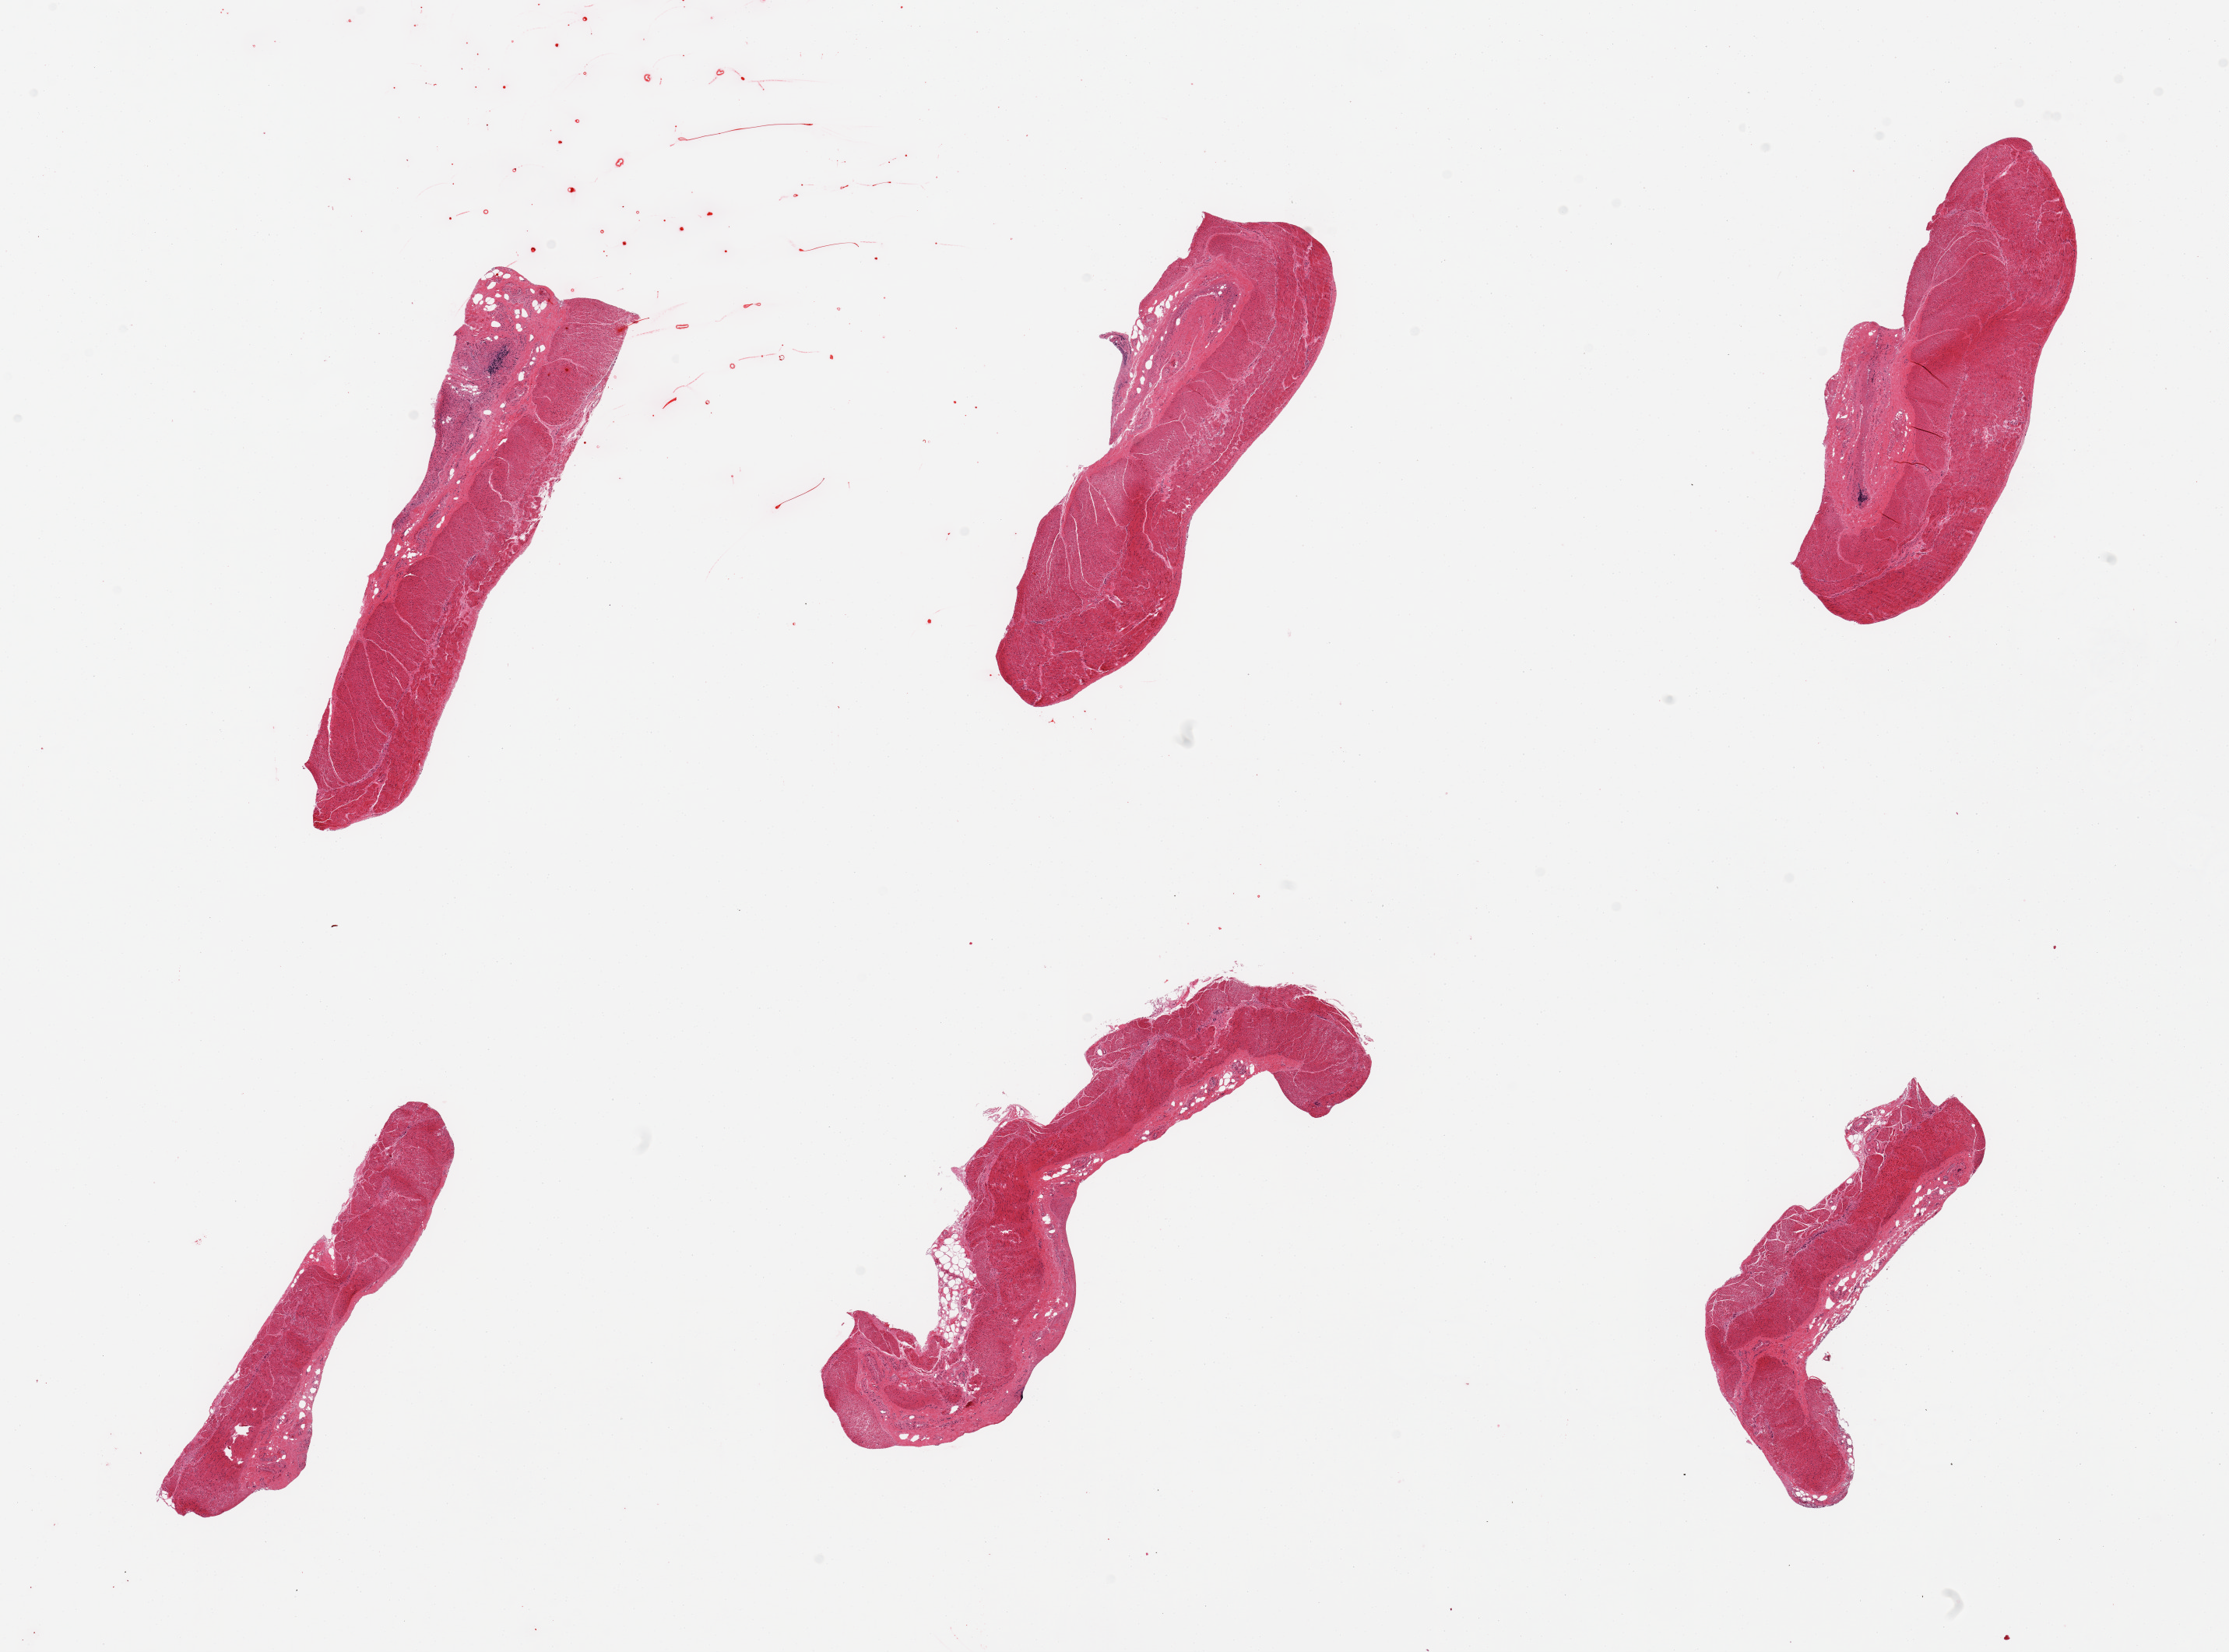
Hematoxylin and eosin (H&E) whole-slide image, low-resolution overview of the scanned area, about 22.6 x 16.8 mm (acquisition: 20x scan), PAXgene-fixed paraffin-embedded (PFPE) section, target tissue: sigmoid colon, tissue donor sample. Female donor.
Pathologist's review note for this sample: 6 pieces, target muscularis, unusually poorly preserved.